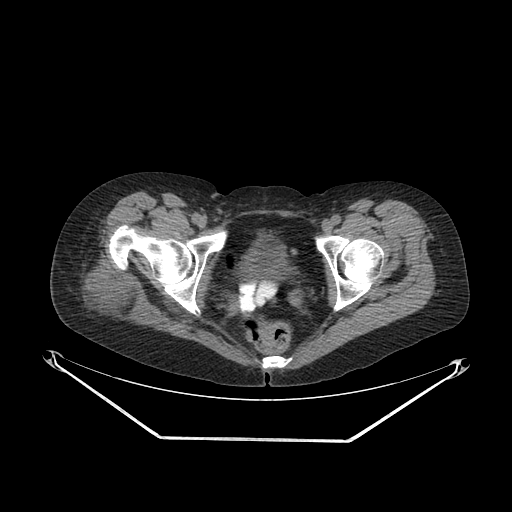
CT of an extremity soft-tissue mass (from a PET/CT study), one axial slice; slice 49 of 267 in the series (ordered by position); soft-tissue window (W 400 / L 40 HU); 3.75 mm slice thickness; 512 × 512 image matrix, field of view 500 × 500 mm. Female patient. Case-level facts recorded for this patient, not image findings: histological type: epithelioid sarcoma with vascular differentiation; site of the primary tumour: right buttock.
Annotated regions visible in this slice (expert contour drawn on MRI and transferred to this co-registered scan by the dataset authors):
- gross tumour volume (mass): bounding box (x1, y1, x2, y2) in pixels: (69, 260, 154, 323)